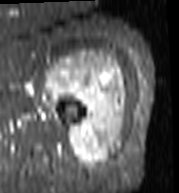
MRI of an extremity soft-tissue mass, one axial slice; position 80 of 103 along the scan axis; STIR; MR volume resampled by the dataset authors to the PET/CT grid (not the native acquisition matrix); 3.27 mm slice thickness; 179 × 193 image matrix, field of view 175 × 188 mm. Female patient. Case-level facts recorded for this patient, not image findings: histological type: undifferentiated – high grade; grade: high; site of the primary tumour: left thigh.
Annotated regions visible in this slice (expert contour drawn on MRI and transferred to this co-registered scan by the dataset authors):
- gross tumour volume including surrounding oedema: bounding box <43,51,126,170> (left, top, right, bottom; pixels)
- gross tumour volume (mass): <45,57,126,170>